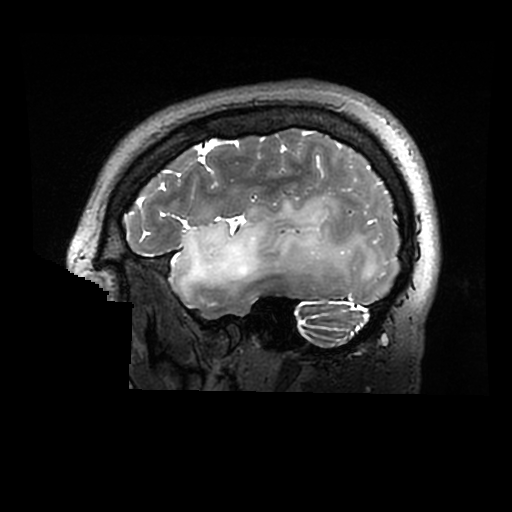
Brain MRI from a brain-tumour surgery series, one sagittal slice. Slice 231 of 320 in the series (ordered by position). 0.6 mm slice thickness. 512 × 512 image matrix, field of view 240 × 240 mm. From the clinical record (not read from this slice): histopathology: Astrocytoma; WHO grade: 2; IDH mutation: yes.
Outlined on this slice (manually delineated by an expert):
- tumour: box from (x=170, y=195) to (x=378, y=297) px